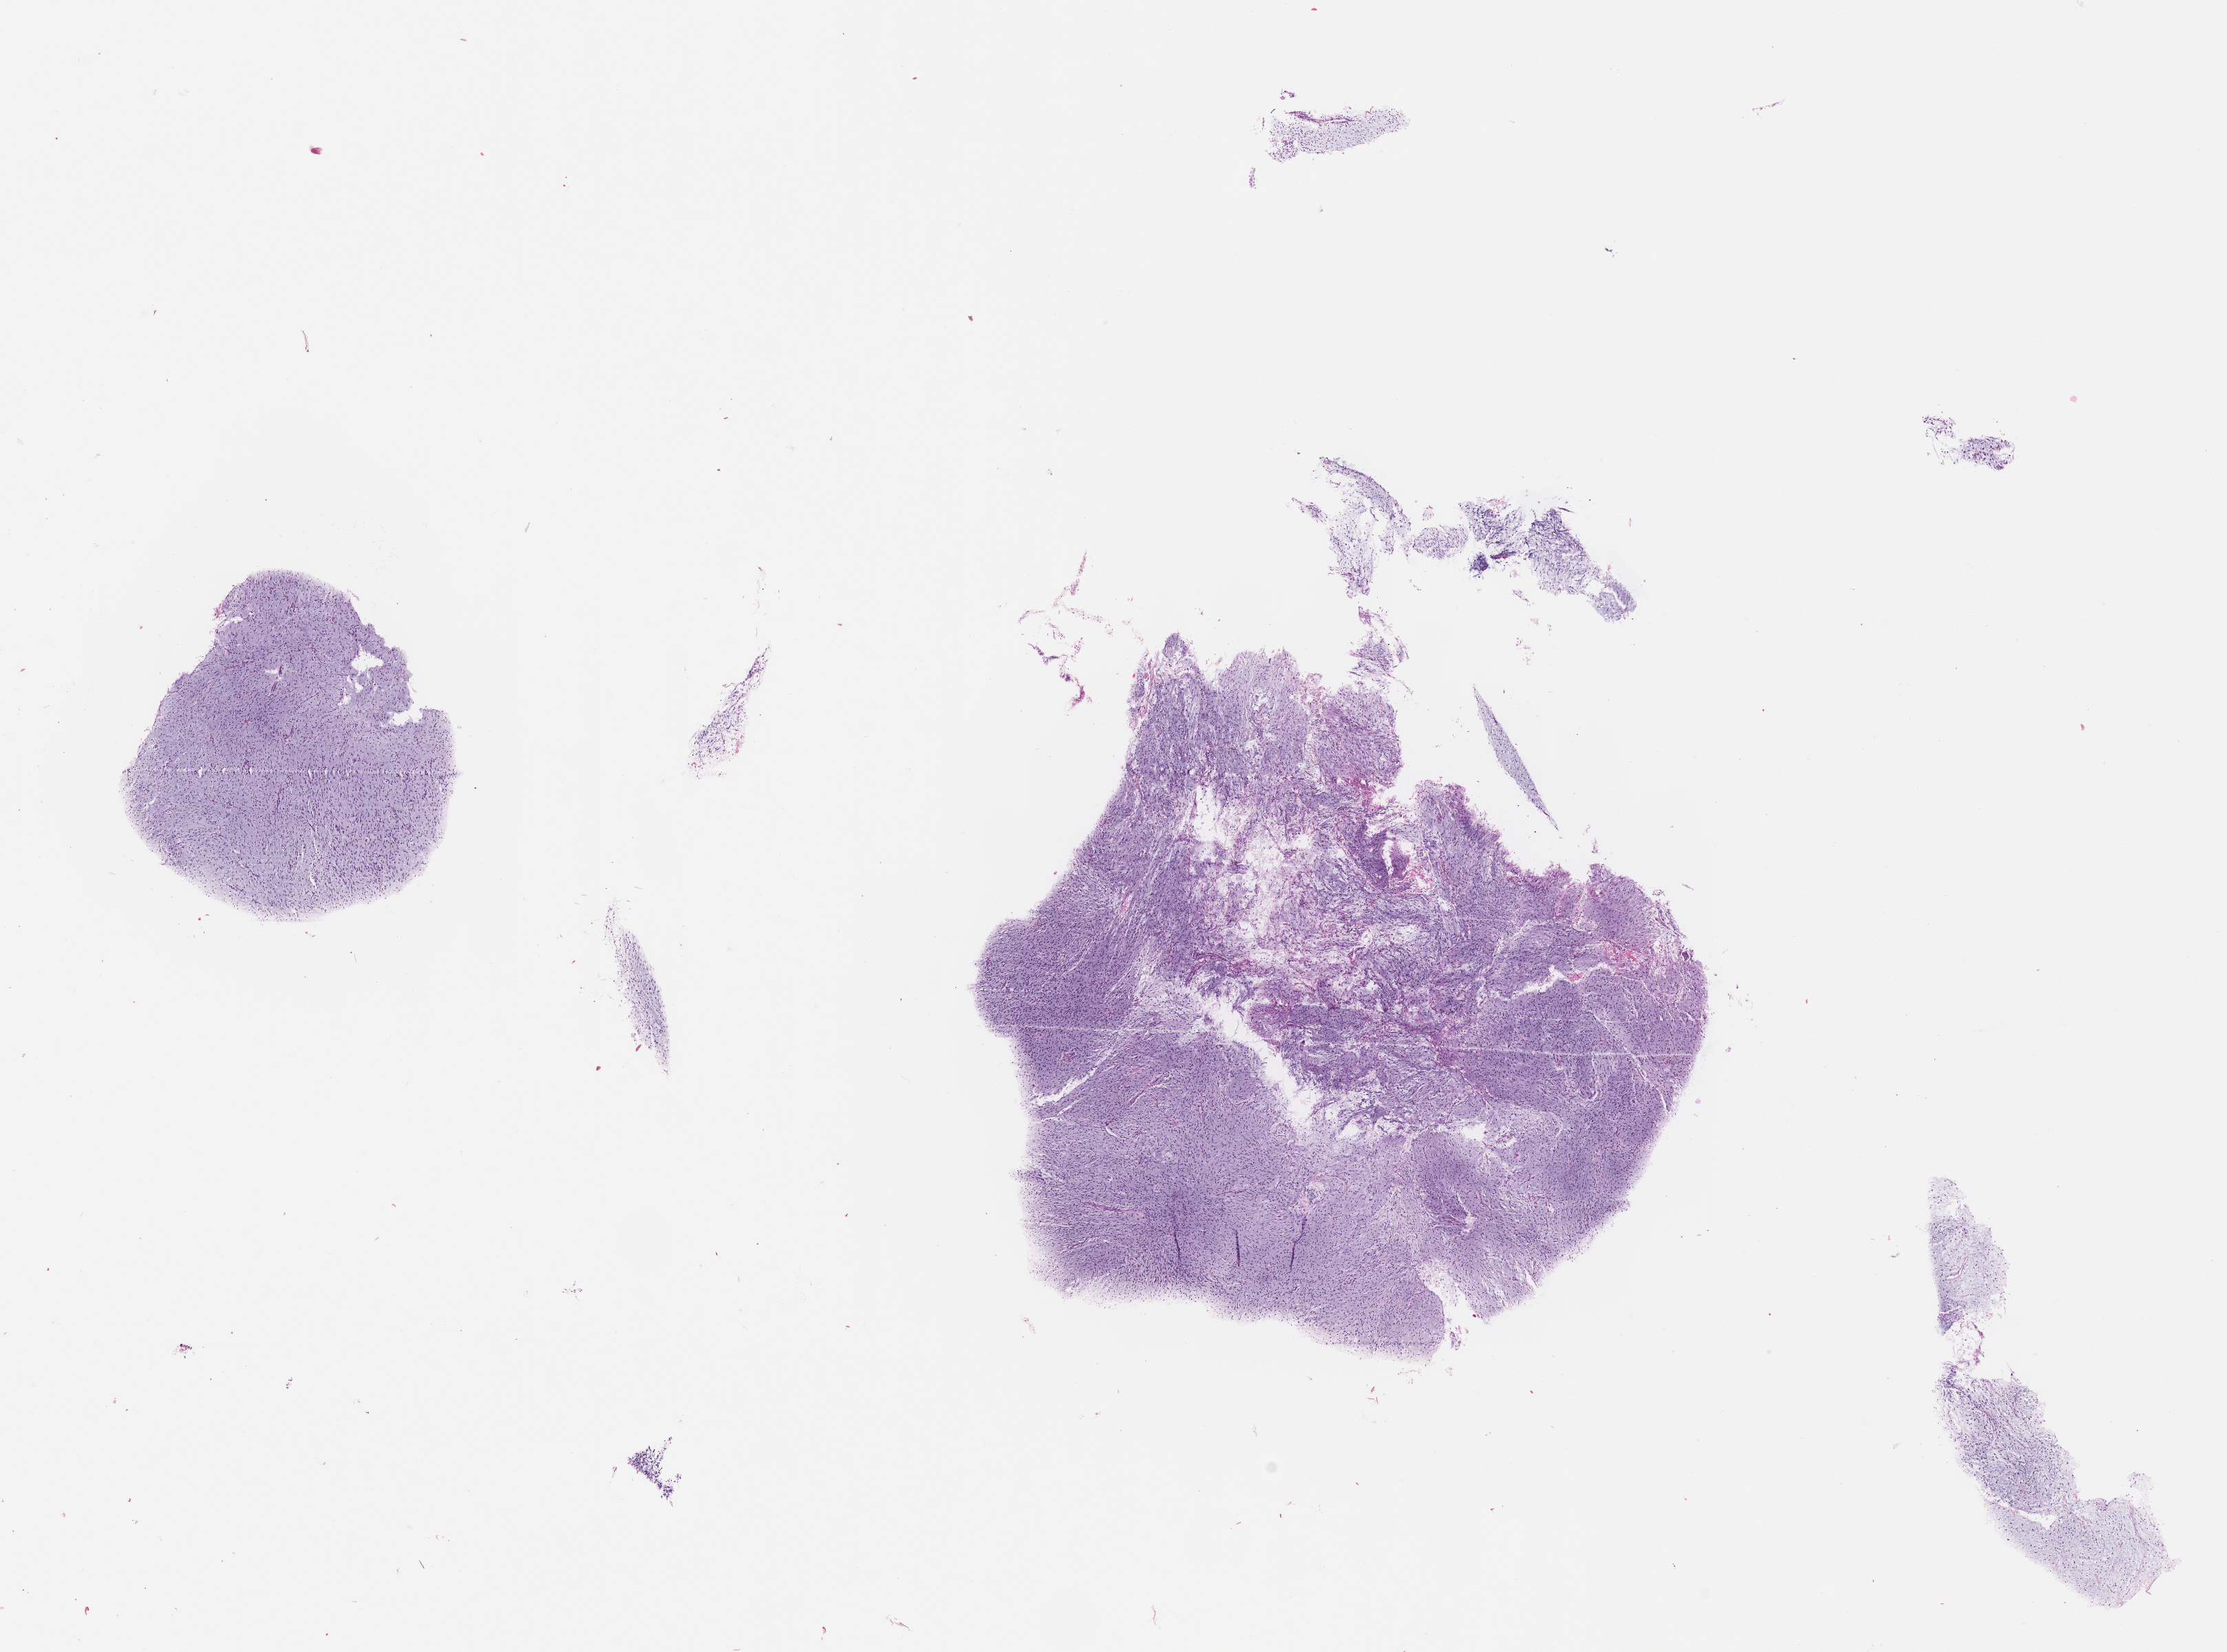
H&E whole-slide image of tumor tissue — shown as a low-resolution overview of the whole scanned area (about 13.1 x 9.7 mm). Formalin-fixed, paraffin-embedded (FFPE) tissue. Site: brain. Female patient, age at diagnosis 4.7 years.
Diagnosis: rhabdomyosarcoma; histological classification: embryonal rhabdomyosarcoma.